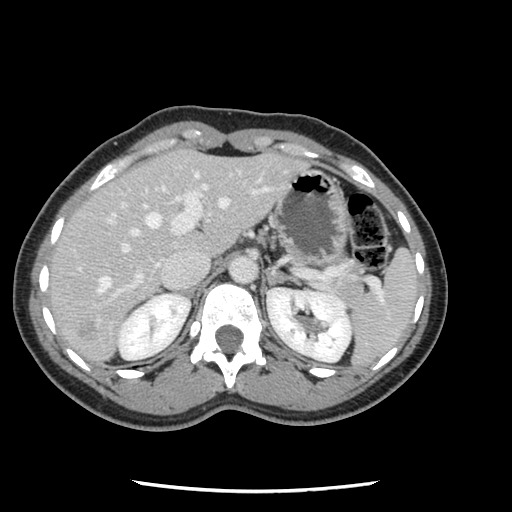
Contrast-enhanced abdominal CT, one axial slice; position 81 of 134 along the scan axis; 120 kVp; intravenous contrast given; soft-tissue window (W 400 / L 40 HU); 2.5 mm slice thickness; 512 × 512 image matrix, field of view 330 × 330 mm. Female patient, age 43 years. Case-level facts recorded for this patient, not image findings: diagnosis: colorectal cancer liver metastases, imaged before liver resection; multiple liver metastases: yes; largest metastasis: 3.4 cm.
Outlined on this slice (outlined manually by an expert reader):
- hepatic veins: box from (x=97, y=172) to (x=230, y=294) px
- liver: (x=49, y=151)–(x=304, y=364)
- planned liver remnant (the part of the liver to remain after resection): (x=48, y=155)–(x=190, y=306)
- portal vein (with intrahepatic branches): (x=93, y=184)–(x=272, y=307)
- liver metastasis: (x=75, y=323)–(x=96, y=339)